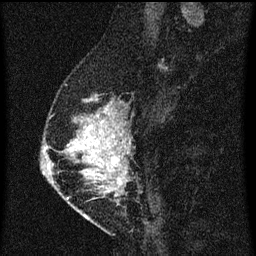
Breast MRI (dynamic contrast-enhanced), one sagittal slice; position 21 of 60 along the scan axis; dynamic contrast-enhanced series, image 2 of 3 at this slice position (ordered by acquisition); 1.5 T; TE 4.2 ms, TR 8 ms; 2 mm slice thickness; 256 × 256 image matrix, field of view 180 × 180 mm. Patient: female, 47 years.
Structures marked on this image (semi-automatically segmented with operator editing):
- analysis volume of interest (the breast-tissue region the enhancement analysis was run in; not a lesion): bounding box [x1, y1, x2, y2] px = [50, 84, 139, 203]
- tumour enhancement mask (voxels above the 70 % enhancement threshold inside the analysis volume of interest): [66, 98, 130, 199]